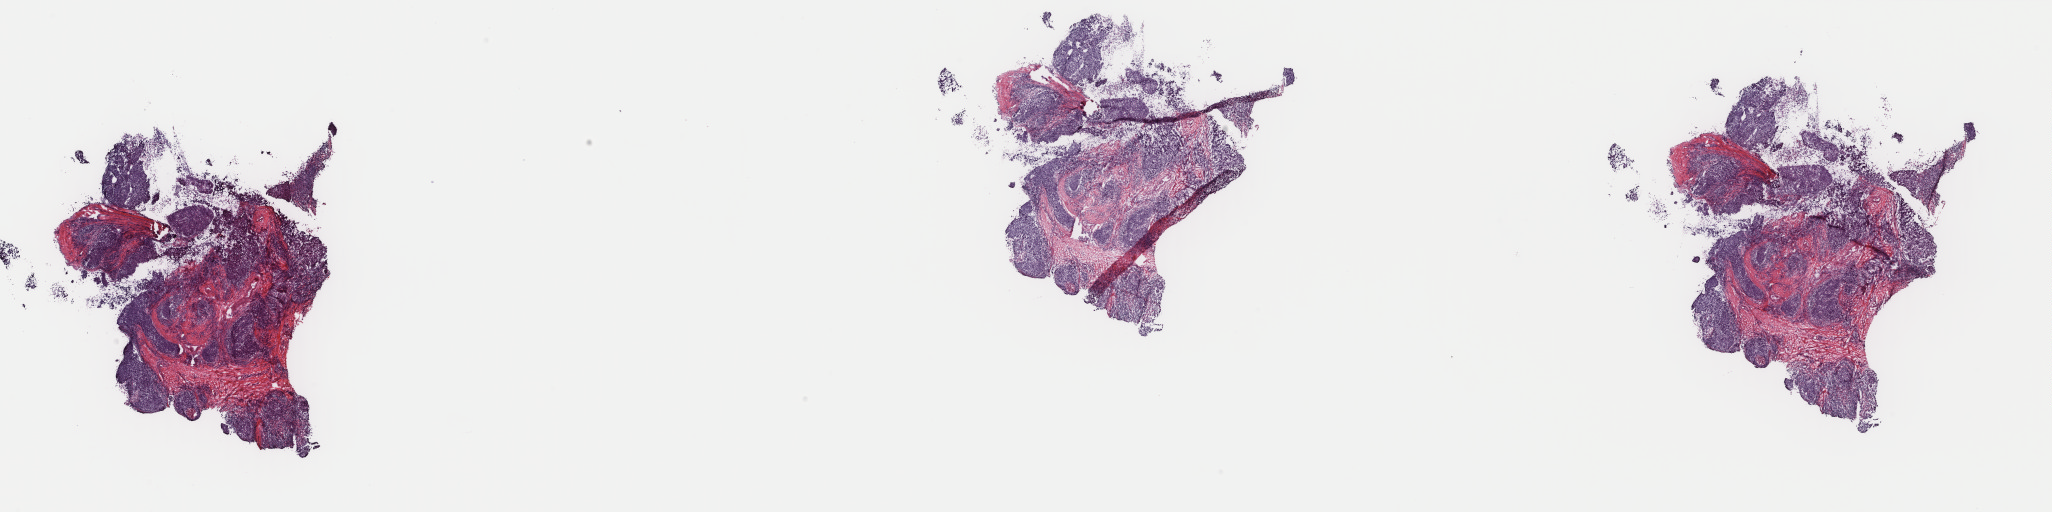
Digitized Hematoxylin and eosin (H&E) stained tissue section (whole slide), low-resolution overview of the scanned area, about 32.6 x 8.1 mm (acquisition: 40x scan). Frozen section. Head and neck, primary tumour sample. Male, age 59 years at initial diagnosis. Pathologist review of this section (percent, as recorded): tumour cells 100%, tumour nuclei 75%.
Histologic diagnosis: Squamous cell carcinoma, NOS.